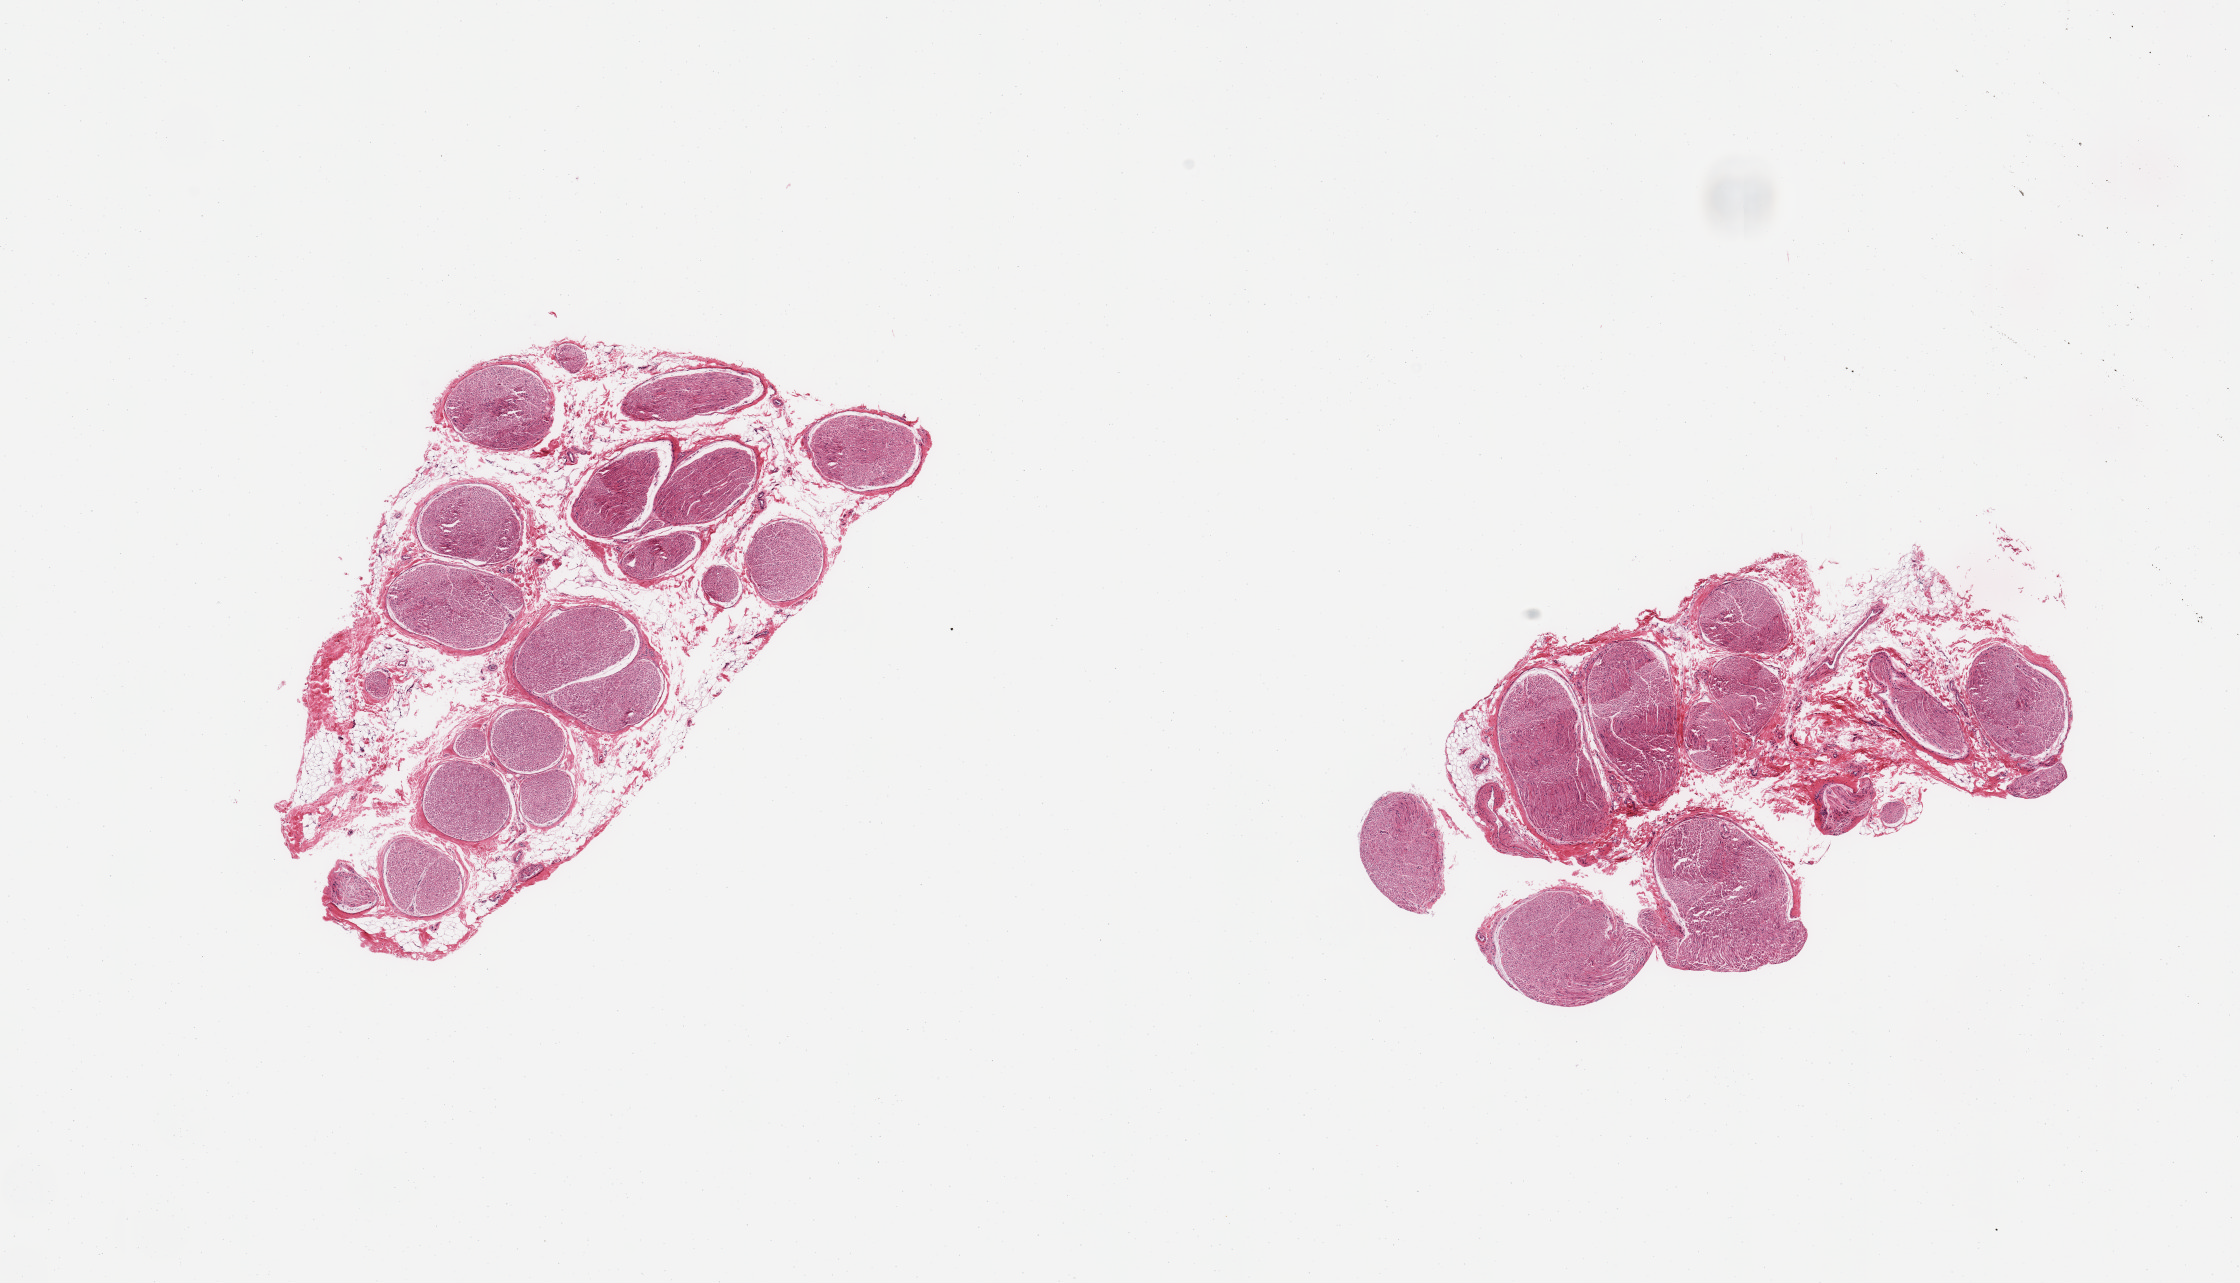
Whole-slide image, hematoxylin and eosin (H&E) stain — low-resolution overview of the scanned area, about 17.7 x 10.1 mm (slide scanned at 20x); PAXgene-fixed paraffin-embedded (PFPE) section; section of tibial nerve (target tissue); tissue donor sample.
• review note (as recorded): 2 pieces; 20% and 10% internal fat